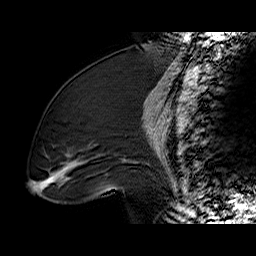
Breast MRI (dynamic contrast-enhanced), one sagittal slice. Dynamic contrast-enhanced series, time point 2 of 6 at this slice position (early post-contrast). 1.5 T. TE 6.2 ms, TR 32.4 ms. 4 mm slice thickness. 256 × 256 image matrix, field of view 200 × 200 mm. Female patient. Case-level facts recorded for this patient, not image findings: setting: breast cancer imaged before/during neoadjuvant chemotherapy; receptor status: triple-negative.
Structures marked on this image (semi-automatic segmentation, software-assisted and operator-edited):
- analysis volume of interest (the breast-tissue region the enhancement analysis was run in; not a lesion): bounding box (x1, y1, x2, y2) in pixels: (36, 97, 134, 196)
- tumour enhancement mask (voxels above the 100 % enhancement threshold inside the analysis volume of interest): (51, 160, 126, 183)